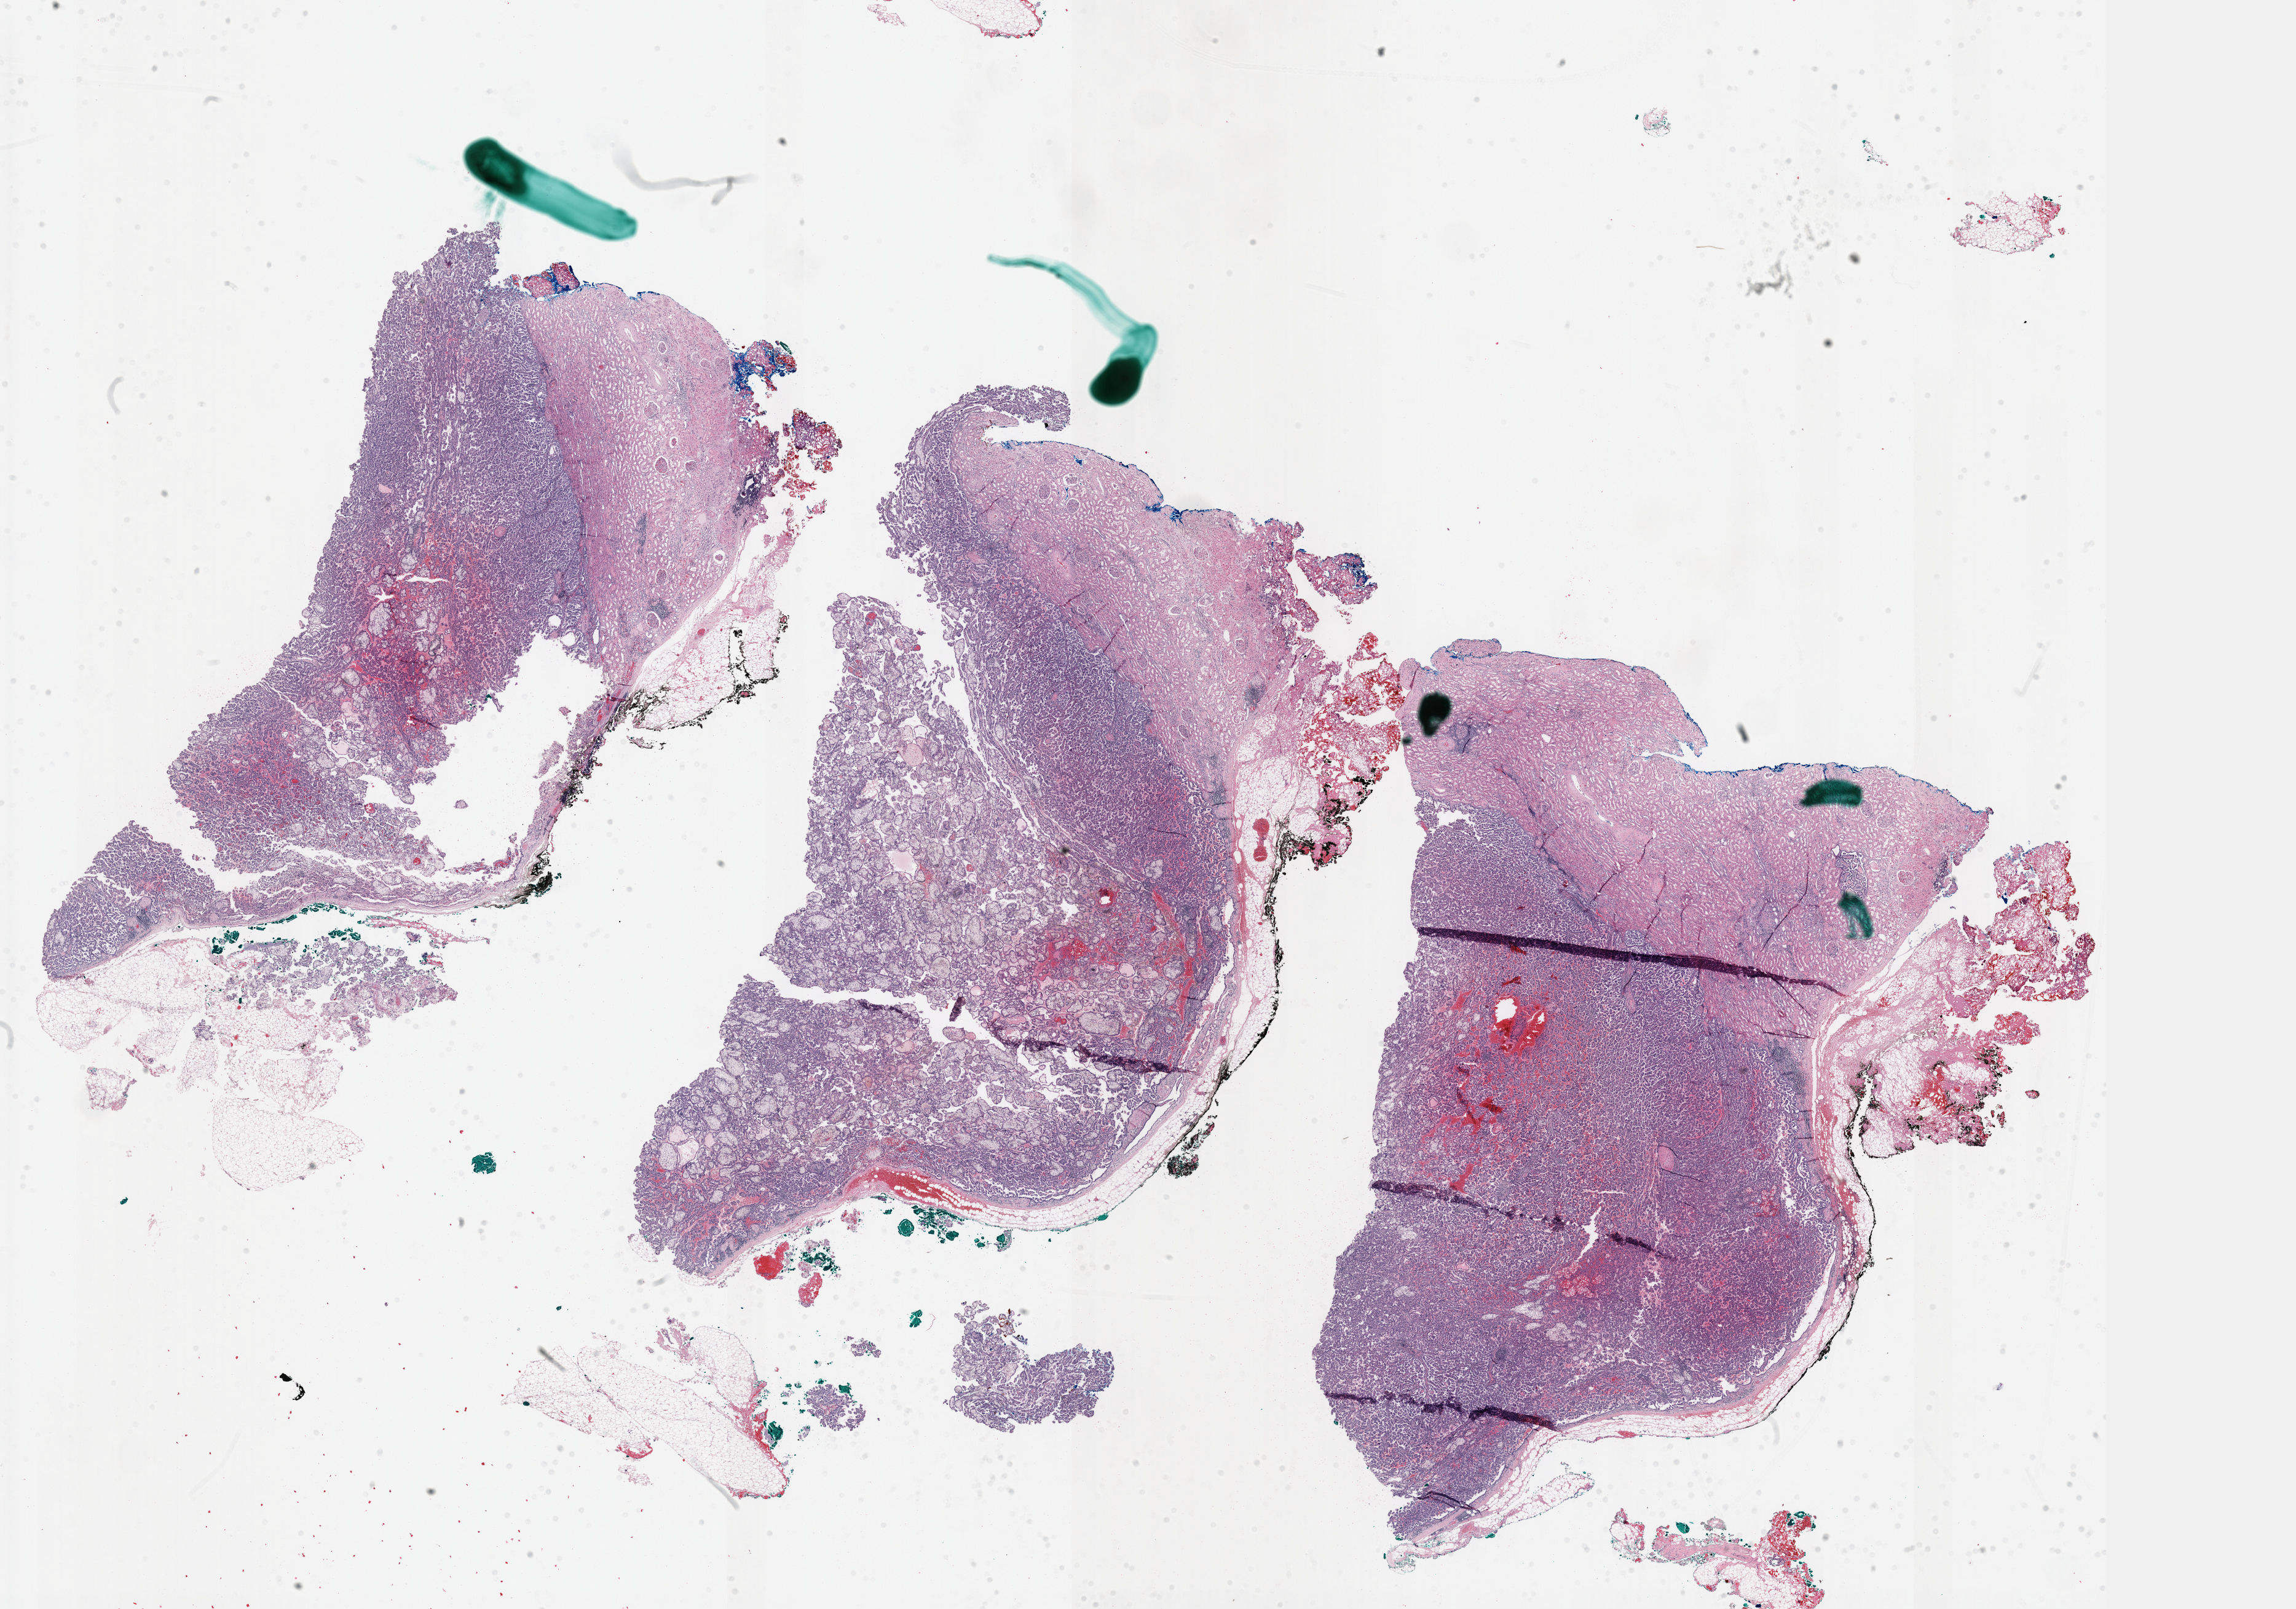
Whole-slide histology image, H&E-stained — a low-resolution overview of the entire scanned area, about 30.2 x 21.1 mm (slide scanned at 40x), formalin-fixed paraffin-embedded (FFPE) diagnostic section, kidney, primary tumour sample. Patient: male, age at initial diagnosis 65 years.
Histologic diagnosis: Papillary adenocarcinoma, NOS.